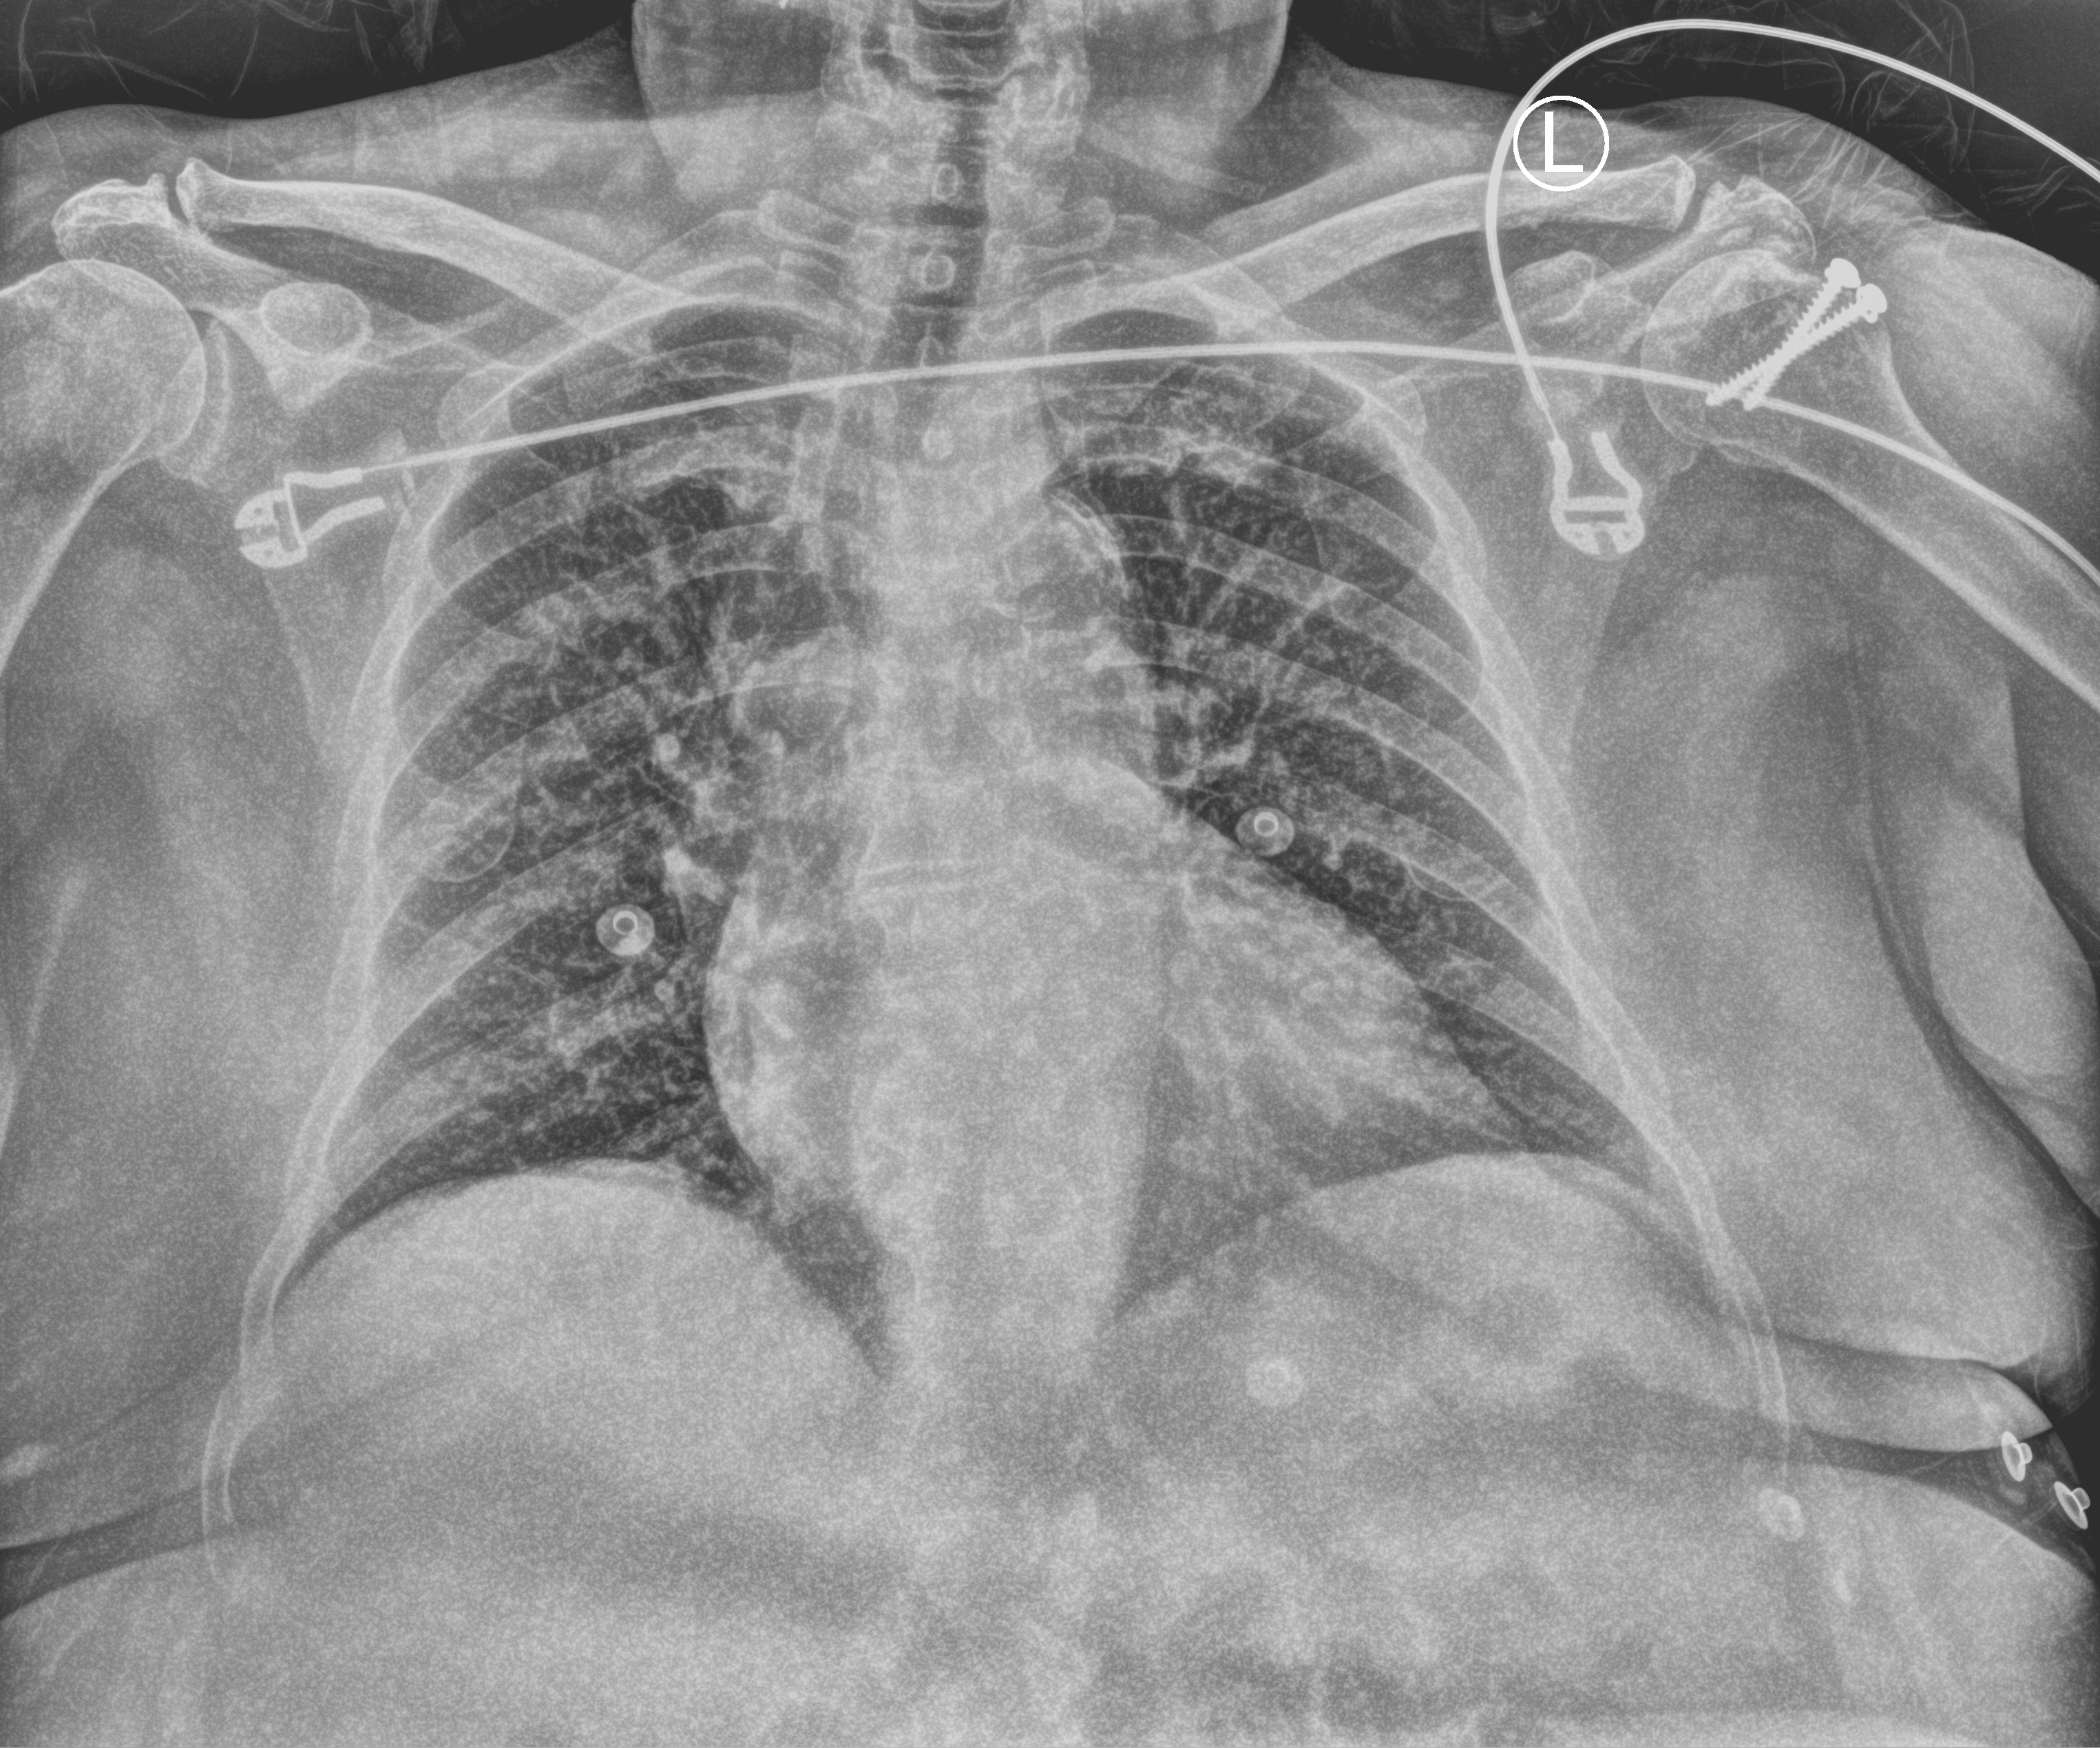
Chest X-ray (portable); anteroposterior (AP) projection. Patient hospitalised with COVID-19; female, aged 60–74 years.
From the hospital-stay record, not from the radiograph (when in the stay this image was taken is not recorded): mechanically ventilated during this hospital stay: no; length of hospital stay: 13 days; admitted to intensive care during this hospital stay: no.